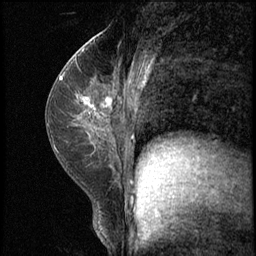
Breast MRI (dynamic contrast-enhanced), one sagittal slice. Slice 33 of 62 in the series (ordered by position). 3 images stored at this slice position (order not interpretable as contrast timing). 1.5 T. TE 4.2 ms, TR 8.7 ms. 2.5 mm slice thickness. 256 × 256 image matrix, field of view 180 × 180 mm. Female patient, age 35 years. From the clinical record (not read from this slice): setting: breast cancer imaged before/during neoadjuvant chemotherapy; receptor status: HER2-positive.
Outlined on this slice (semi-automatic segmentation, software-assisted and operator-edited):
- analysis volume of interest (the breast-tissue region the enhancement analysis was run in; not a lesion): bounding box [x1, y1, x2, y2] px = [71, 78, 120, 139]
- tumour enhancement mask (voxels above the 140 % enhancement threshold inside the analysis volume of interest): [76, 97, 111, 105]